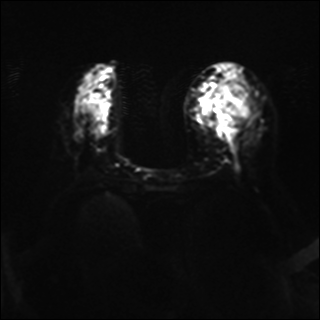
Breast MRI, one axial slice. Position 15 of 37 along the scan axis. Diffusion-weighted series; image 2 of 4 stored at this slice position (different b-values; order by instance number). 1.5 T. 4 mm slice thickness. 320 × 320 image matrix, field of view 320 × 320 mm. Female patient.
Outlined on this slice (outlined manually by an expert reader):
- tumour on diffusion-weighted imaging: bounding box [x1, y1, x2, y2] px = [213, 81, 257, 128]